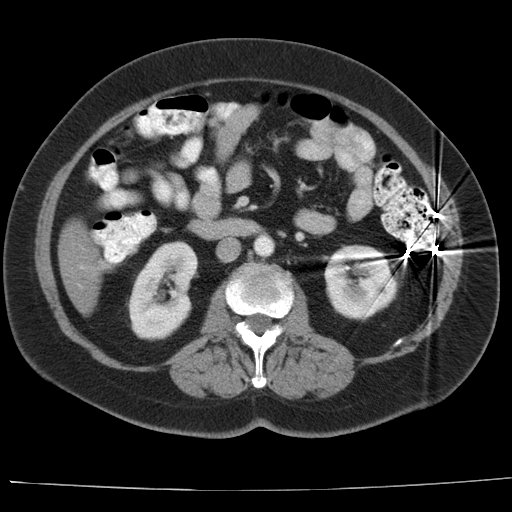
Contrast-enhanced abdominal CT, one axial slice. Position 5 of 44 along the scan axis. 140 kVp. Intravenous contrast given. Soft-tissue window (W 400 / L 40 HU). 512 × 512 image matrix. Female patient. Case-level facts recorded for this patient, not image findings: diagnosis: colorectal cancer liver metastases, imaged before liver resection; multiple liver metastases: yes; largest metastasis: 1.8 cm.
Annotated regions visible in this slice (outlined manually by an expert reader):
- liver: bounding box (x1, y1, x2, y2) in pixels: (60, 220, 101, 313)
- portal vein (with intrahepatic branches): (78, 284, 81, 287)